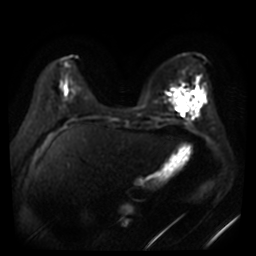
Breast MRI, one axial slice. Position 14 of 44 along the scan axis. Diffusion-weighted series; image 2 of 4 stored at this slice position (different b-values; order by instance number). 3 T. 5 mm slice thickness. 256 × 256 image matrix. Female patient.
Structures marked on this image (outlined manually by an expert reader):
- tumour on diffusion-weighted imaging: bounding box <176,94,196,108> (left, top, right, bottom; pixels)